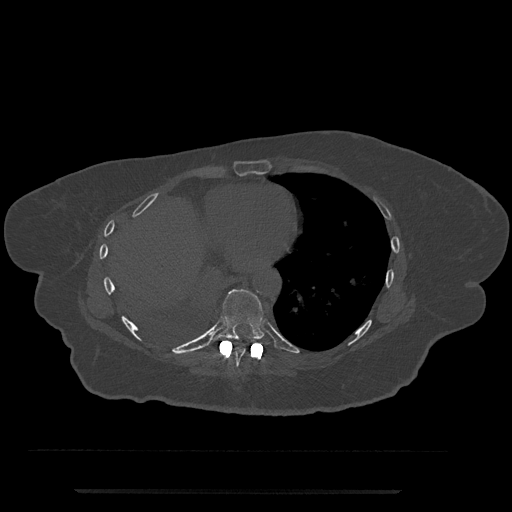
CT including the spine, one axial slice. Reconstruction kernel Br40s/3. 120 kVp. Bone window (W 1800 / L 400 HU). 512 × 512 image matrix, field of view 440 × 440 mm. Female patient, age 51 years. From the clinical record (not read from this slice): primary cancer: neuro.
Outlined on this slice (semi-automatic segmentation, software-assisted and operator-edited):
- T8 vertebra: bounding box [x1, y1, x2, y2] px = [230, 347, 246, 367]
- T9 vertebra: [210, 289, 265, 345]